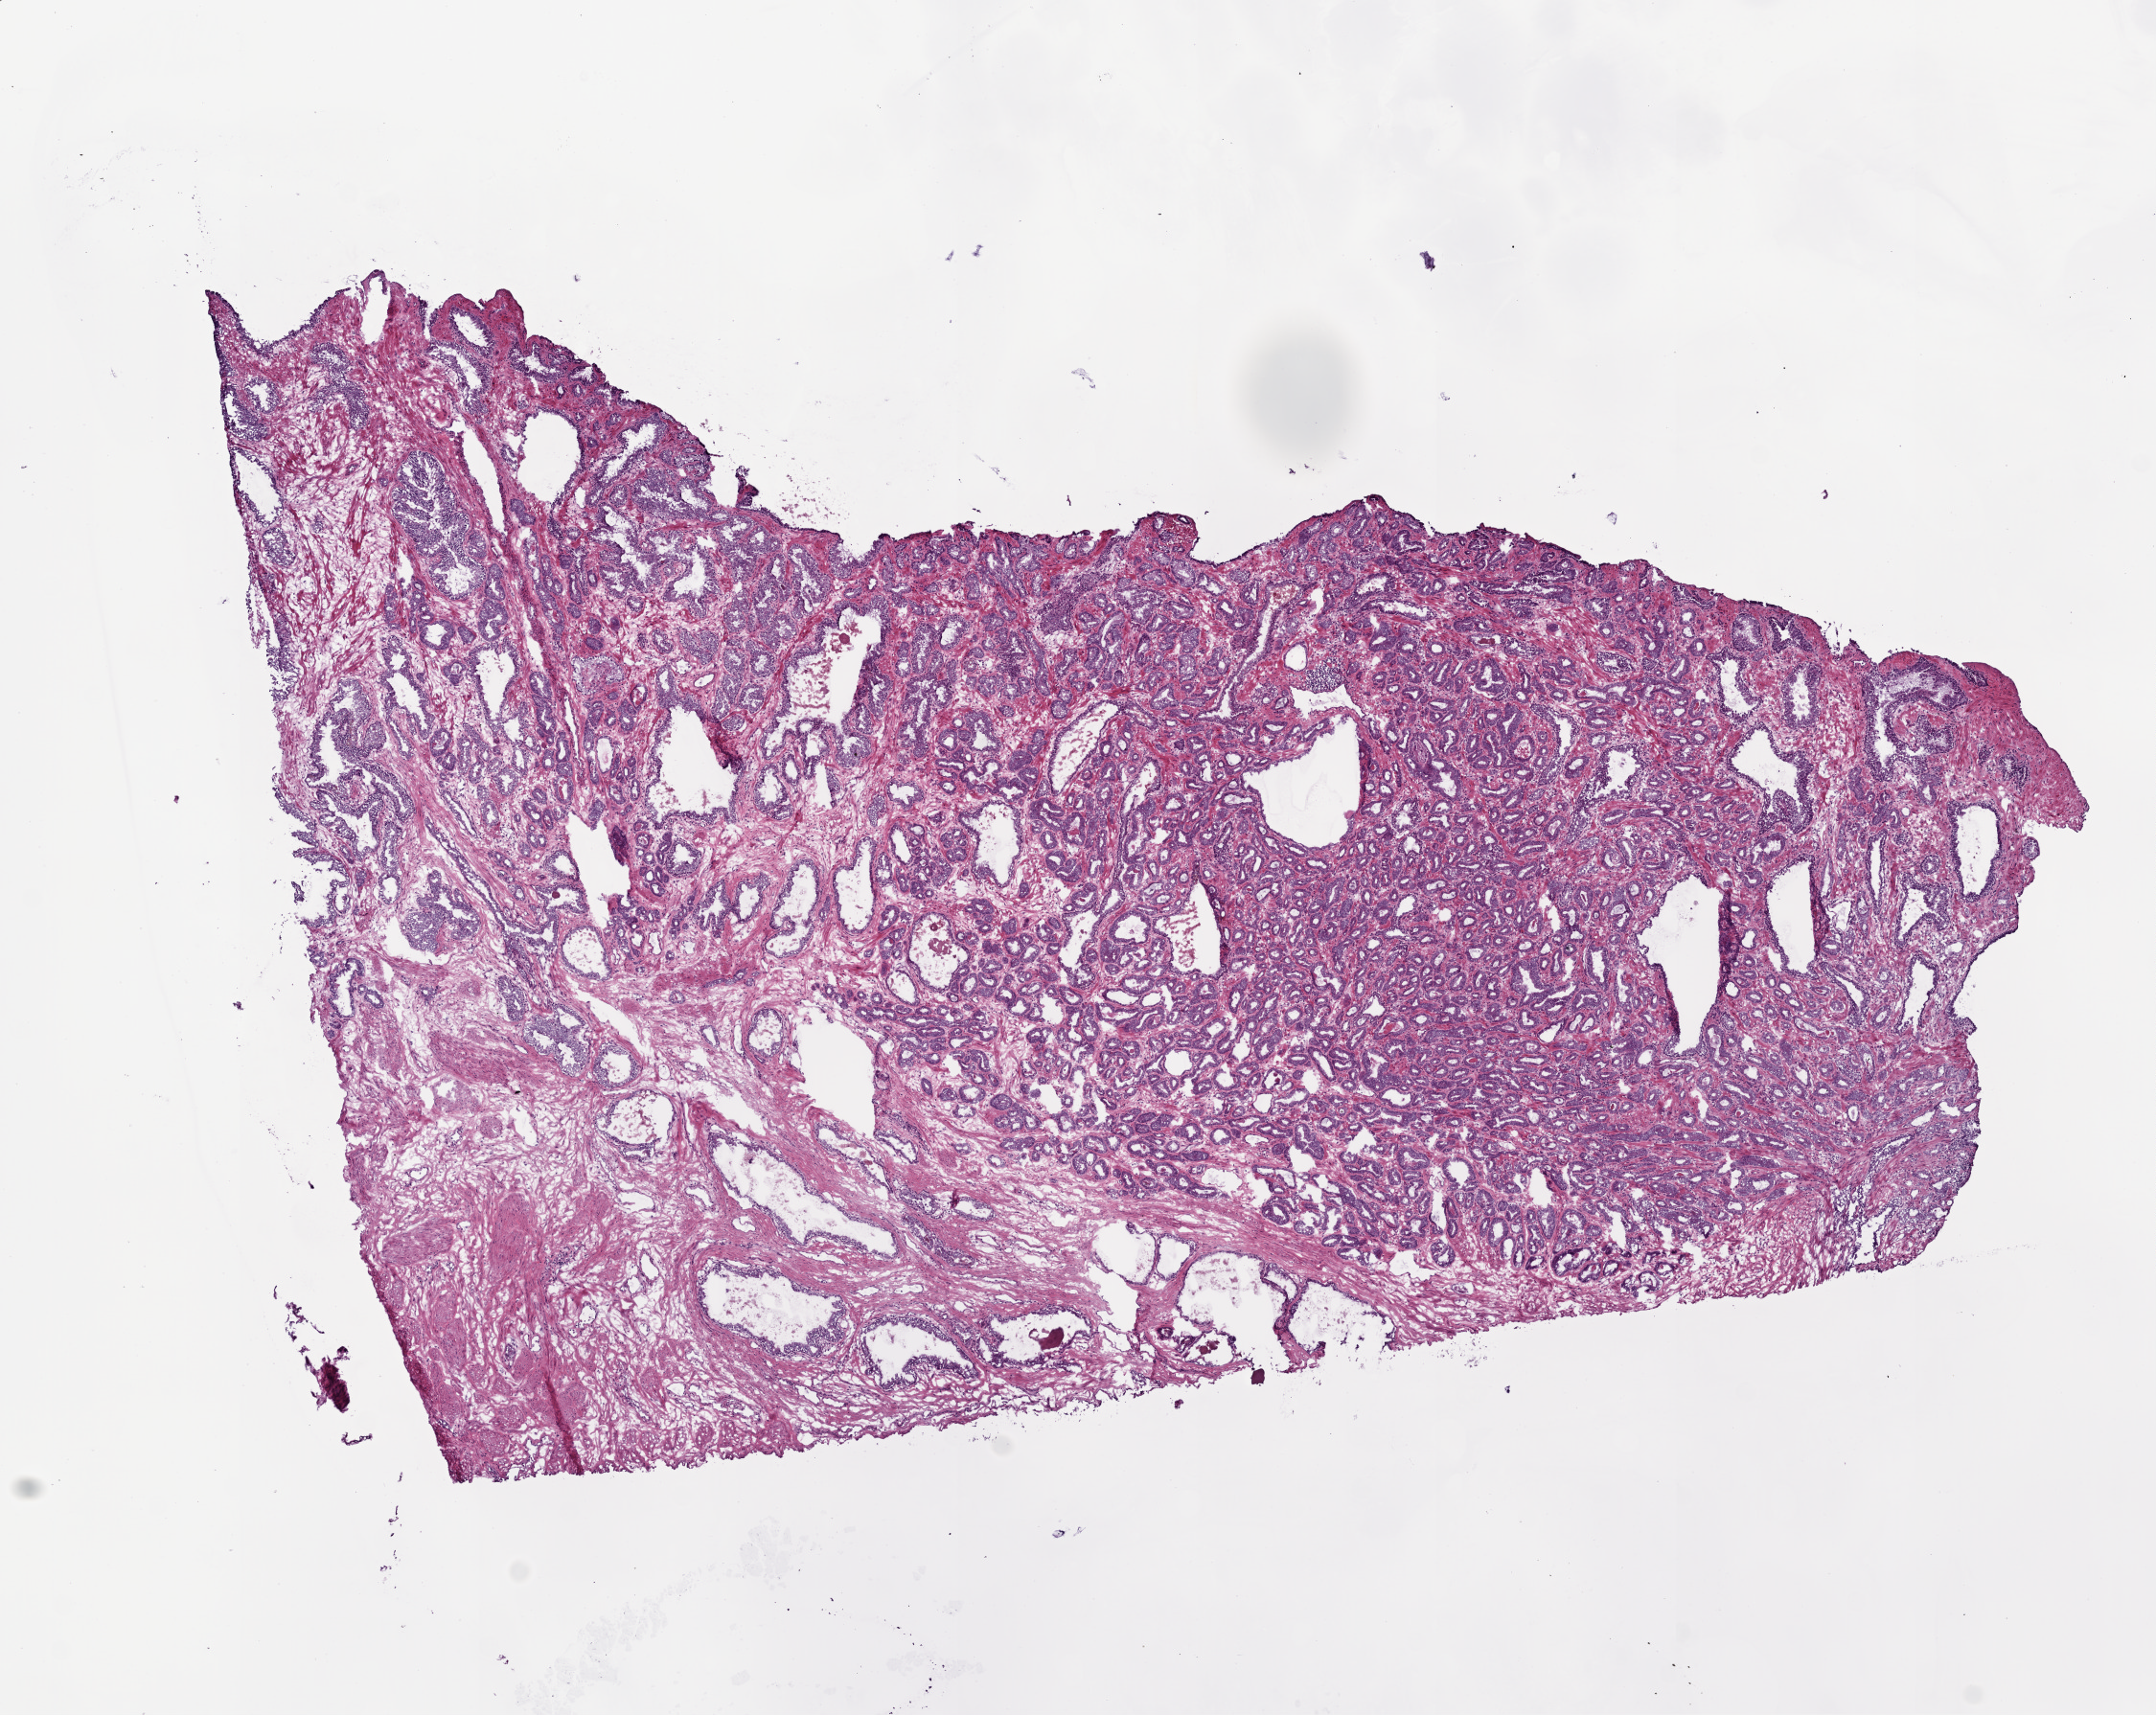
Digitized H&E-stained tissue section (whole slide) — a low-resolution overview of the entire scanned area, about 9.0 x 7.2 mm (slide scanned at 20x). Frozen section from the top of the tissue portion. Sample: primary tumour, prostate. Male patient; age at initial diagnosis 59 years. Pathologist review of this section (percent, as recorded): tumour cells 60%, tumour nuclei 70%.
Diagnosis: Acinar cell carcinoma (prostate gland).